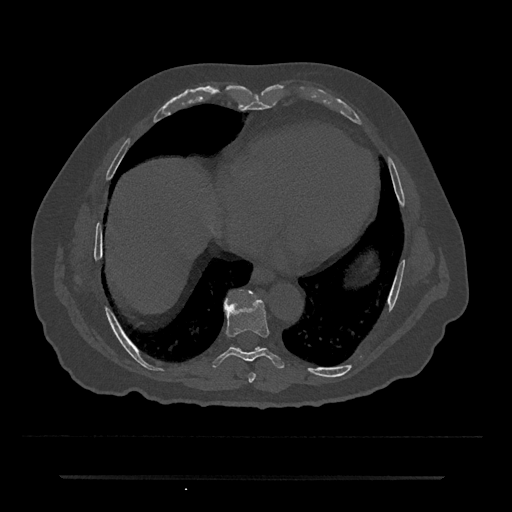
CT including the spine, one axial slice; slice 326 of 797 in the series (ordered by position); reconstruction kernel Br40s/3; 120 kVp; bone window (W 1800 / L 400 HU); 0.5 mm slice thickness; 512 × 512 image matrix, field of view 437 × 437 mm. Male patient, age 69 years. From the clinical record (not read from this slice): primary cancer: prostate.
Structures marked on this image (semi-automatic segmentation, software-assisted and operator-edited):
- T7 vertebra: box from (x=248, y=373) to (x=256, y=383) px
- T8 vertebra: (x=212, y=298)–(x=284, y=369)